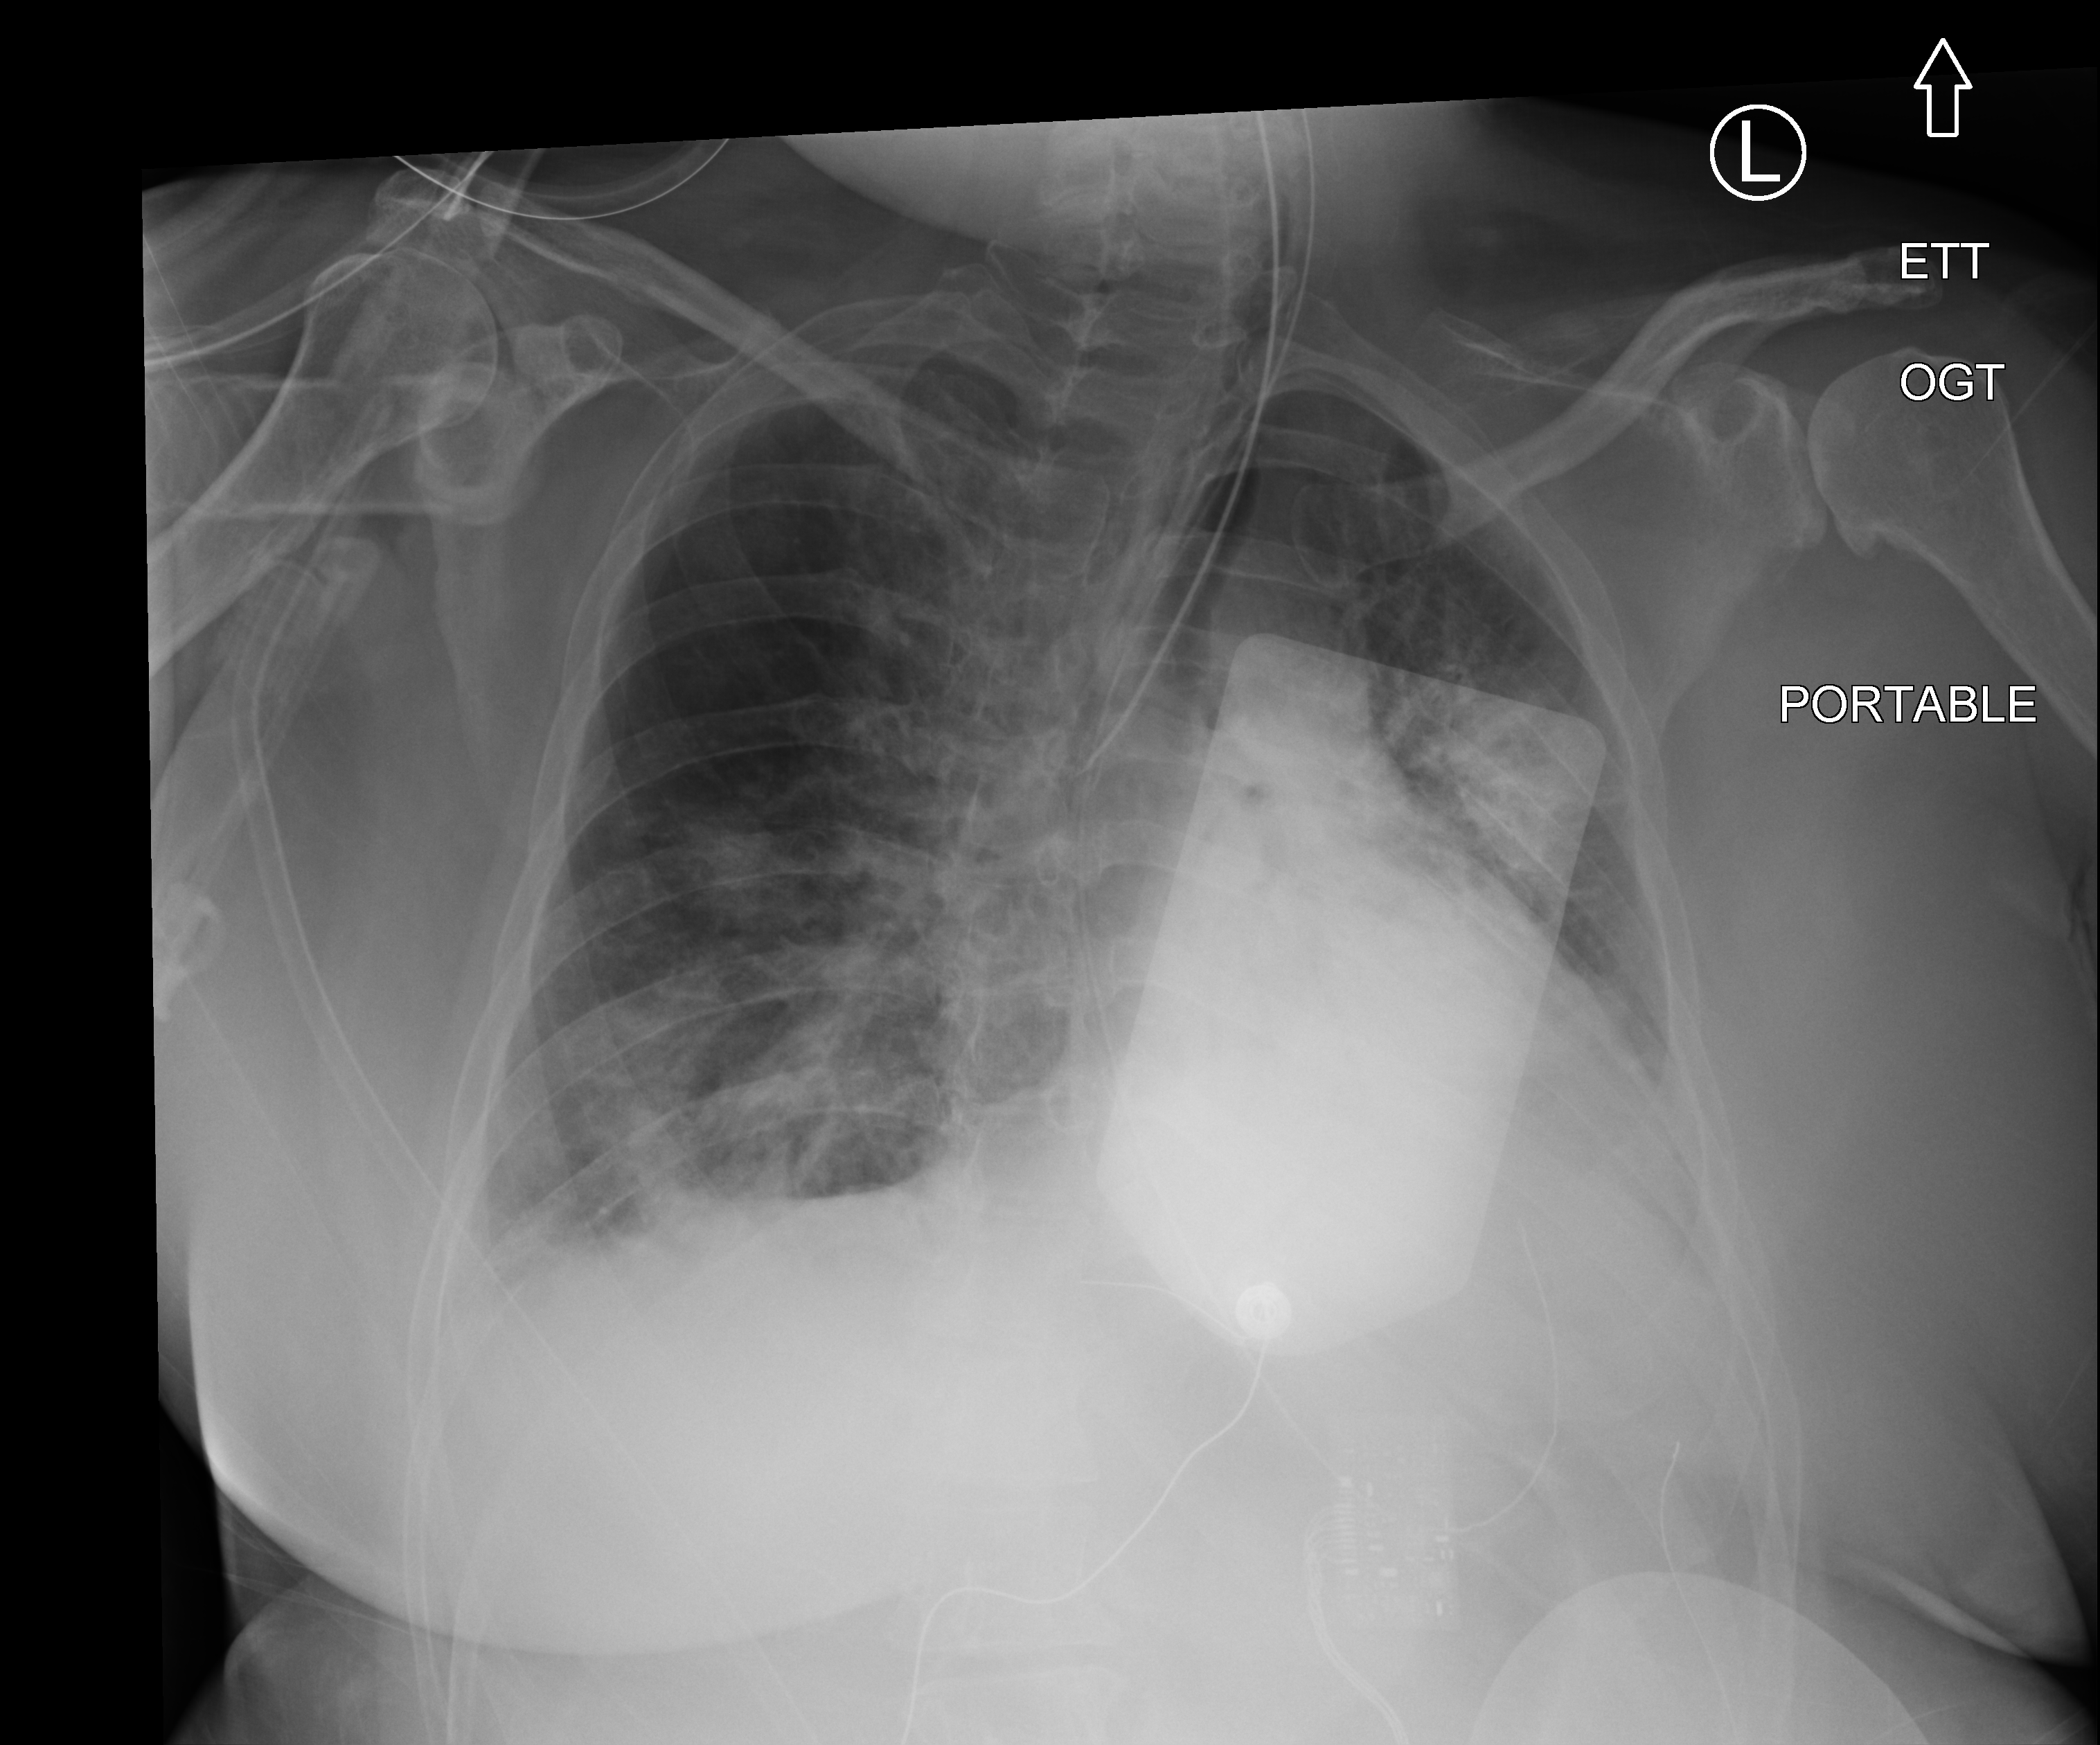
Portable chest radiograph, anteroposterior (AP) projection. Adult patient hospitalised with COVID-19, age 18–59 years.
Hospital-stay facts (about this admission, not read from this image; timing relative to this image not recorded): admitted to intensive care during this hospital stay: yes; mechanically ventilated during this hospital stay: yes.